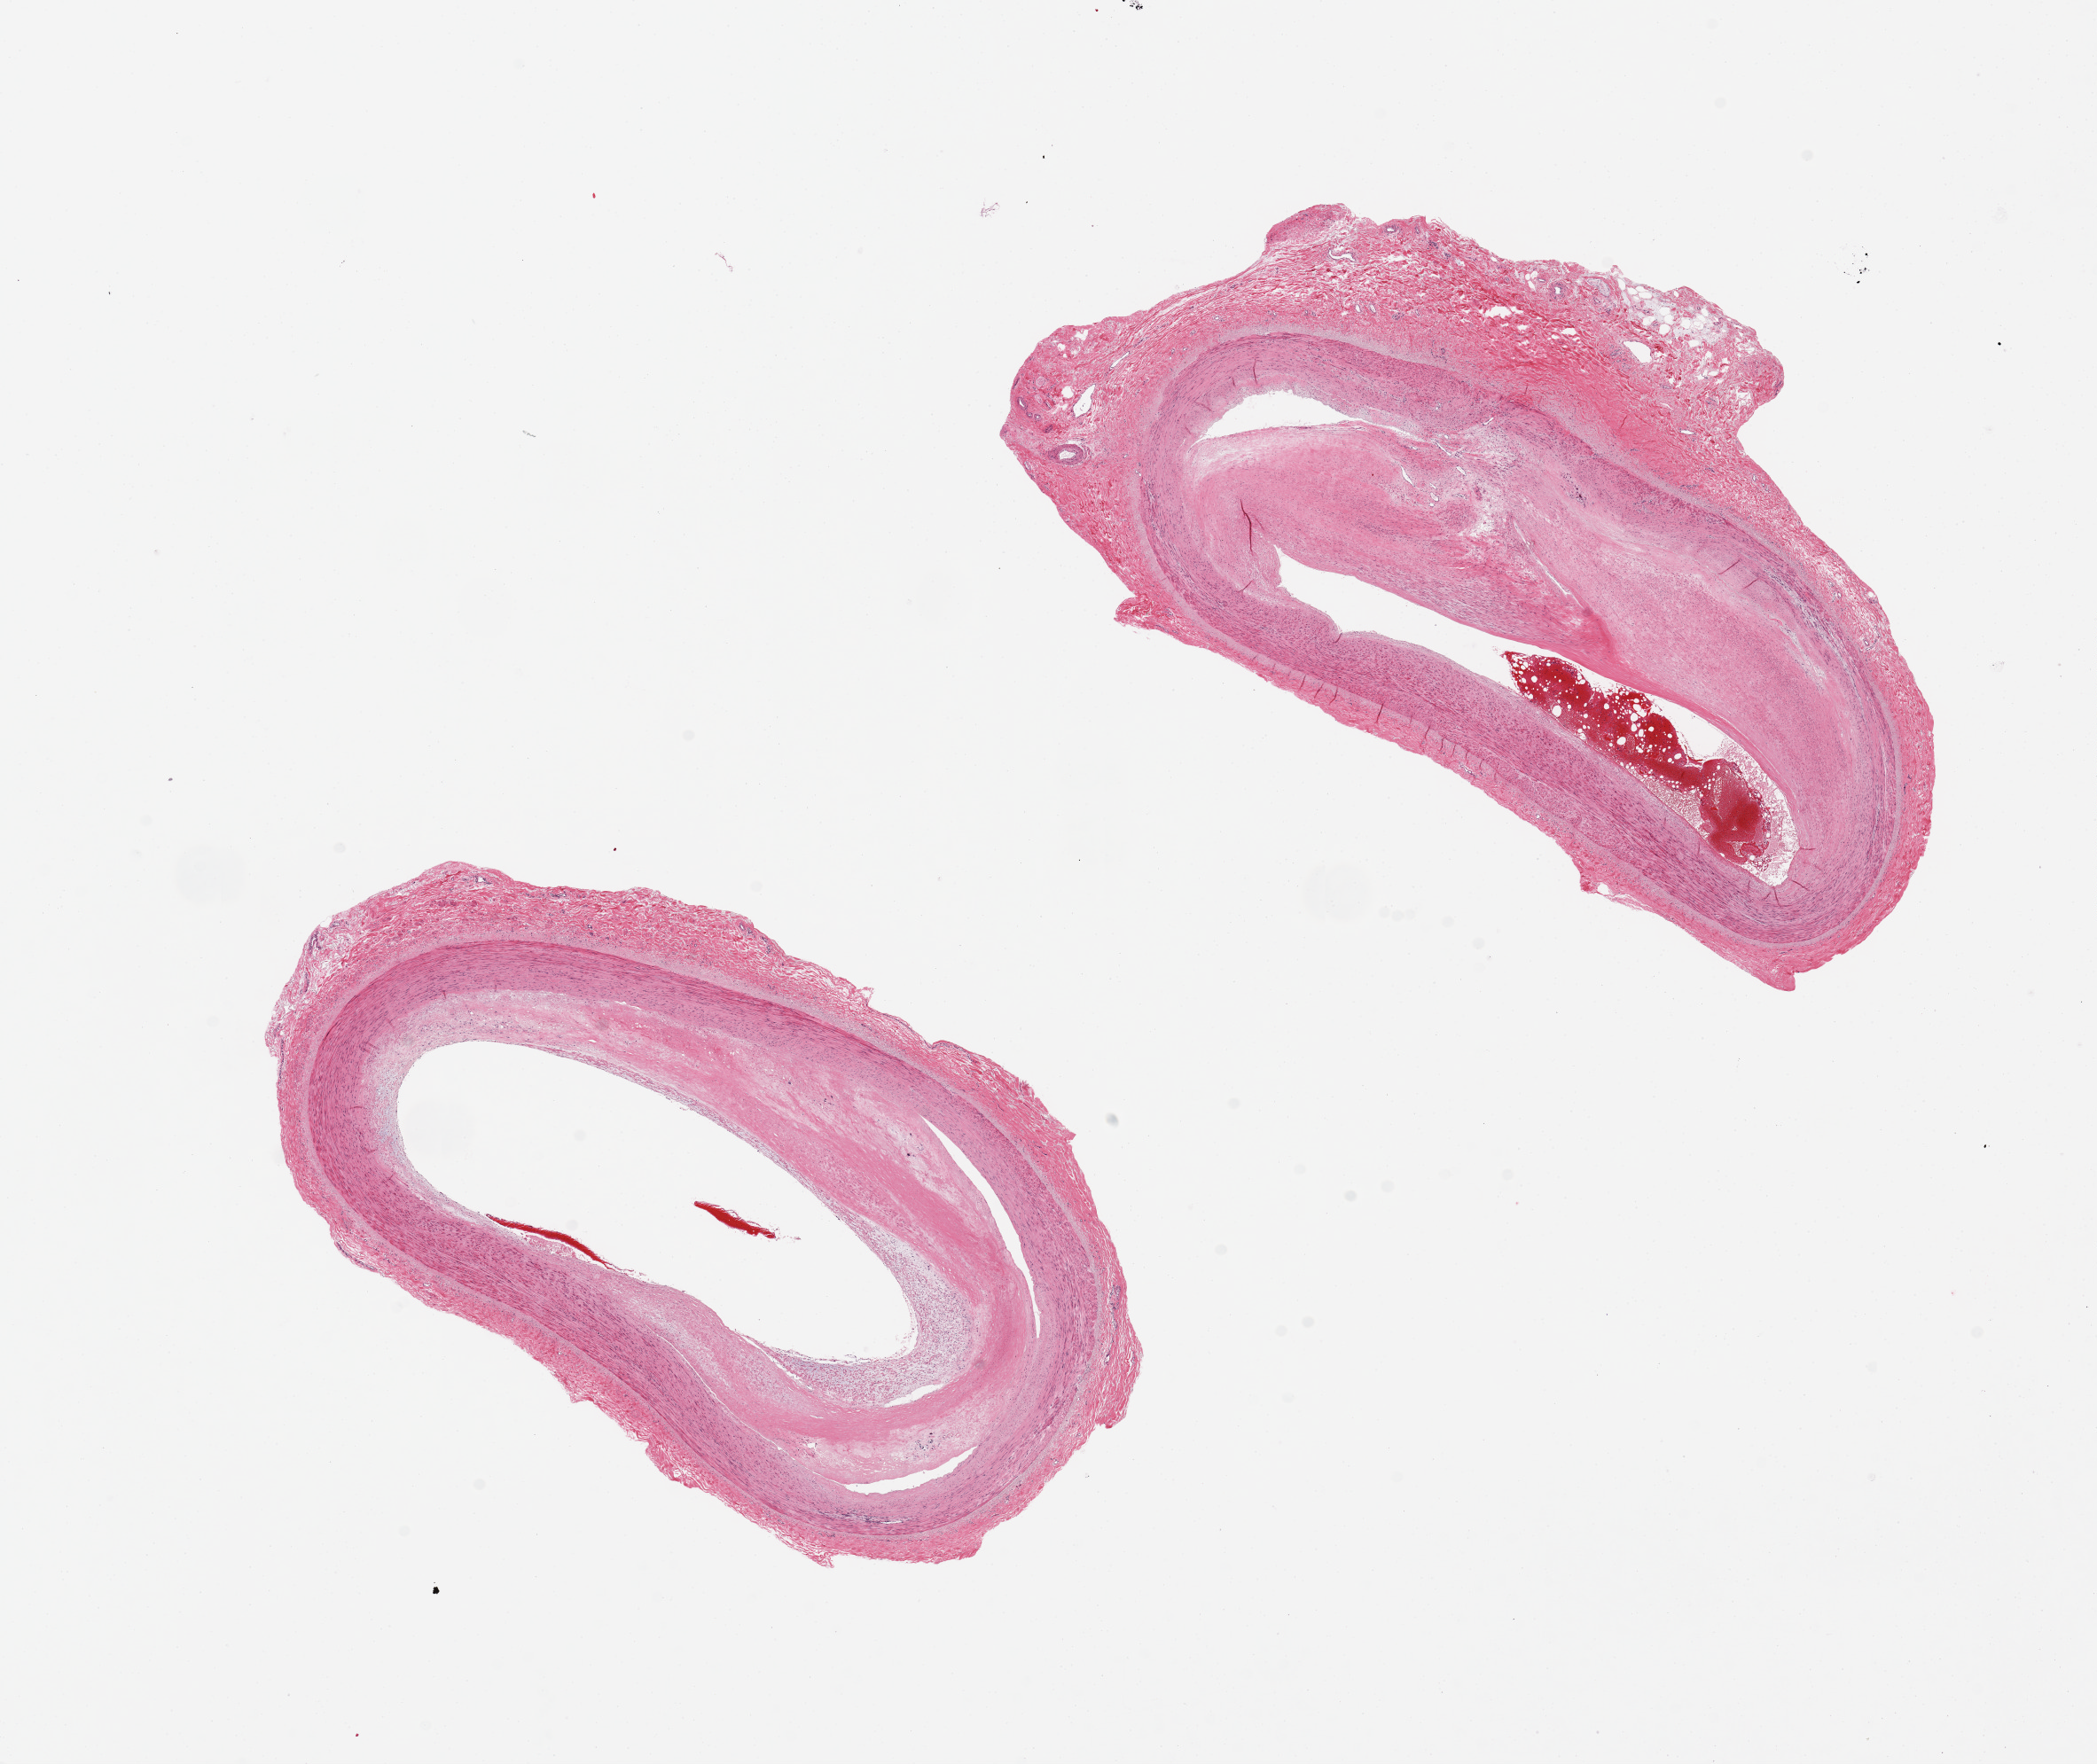
Whole-slide image, hematoxylin and eosin (H&E) stain, whole scanned area (about 18.7 x 15.7 mm) shown as a low-resolution overview; PAXgene-fixed, paraffin-embedded tissue; sampled site (target tissue): tibial artery; donor tissue sample. Donor: male.
Reviewer comment on this tissue sample: 2 pieces, 8.5x5 & 9x5mm; discontinuous adherent fims of fibrous tissue on both up to 1.1mm. 60-70% occlusive atheroscerosis.